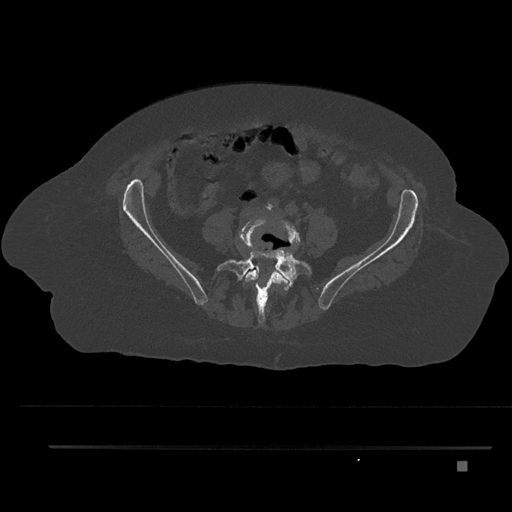
CT including the spine, one axial slice; slice 53 of 797 in the series (ordered by position); reconstruction kernel Br40s/3; 120 kVp; bone window (W 1800 / L 400 HU); 0.5 mm slice thickness; 512 × 512 image matrix, field of view 437 × 437 mm. Patient: female, 76 years. From the clinical record (not read from this slice): primary cancer: lung.
Structures marked on this image (semi-automatic segmentation, software-assisted and operator-edited):
- L4 vertebra: box from (x=239, y=216) to (x=300, y=310) px
- L5 vertebra: (x=216, y=236)–(x=312, y=324)